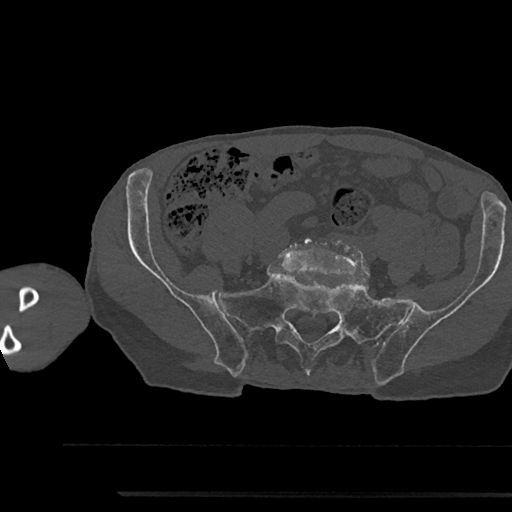
CT including the spine, one axial slice. Slice 301 of 797 in the series (ordered by position). 120 kVp. Bone window (W 1800 / L 400 HU). 0.5 mm slice thickness. 512 × 512 image matrix, field of view 367 × 367 mm. Patient: male, 79 years. From the clinical record (not read from this slice): primary cancer: prostate.
Structures marked on this image (semi-automatic segmentation, software-assisted and operator-edited):
- L5 vertebra: box from (x=279, y=237) to (x=369, y=275) px